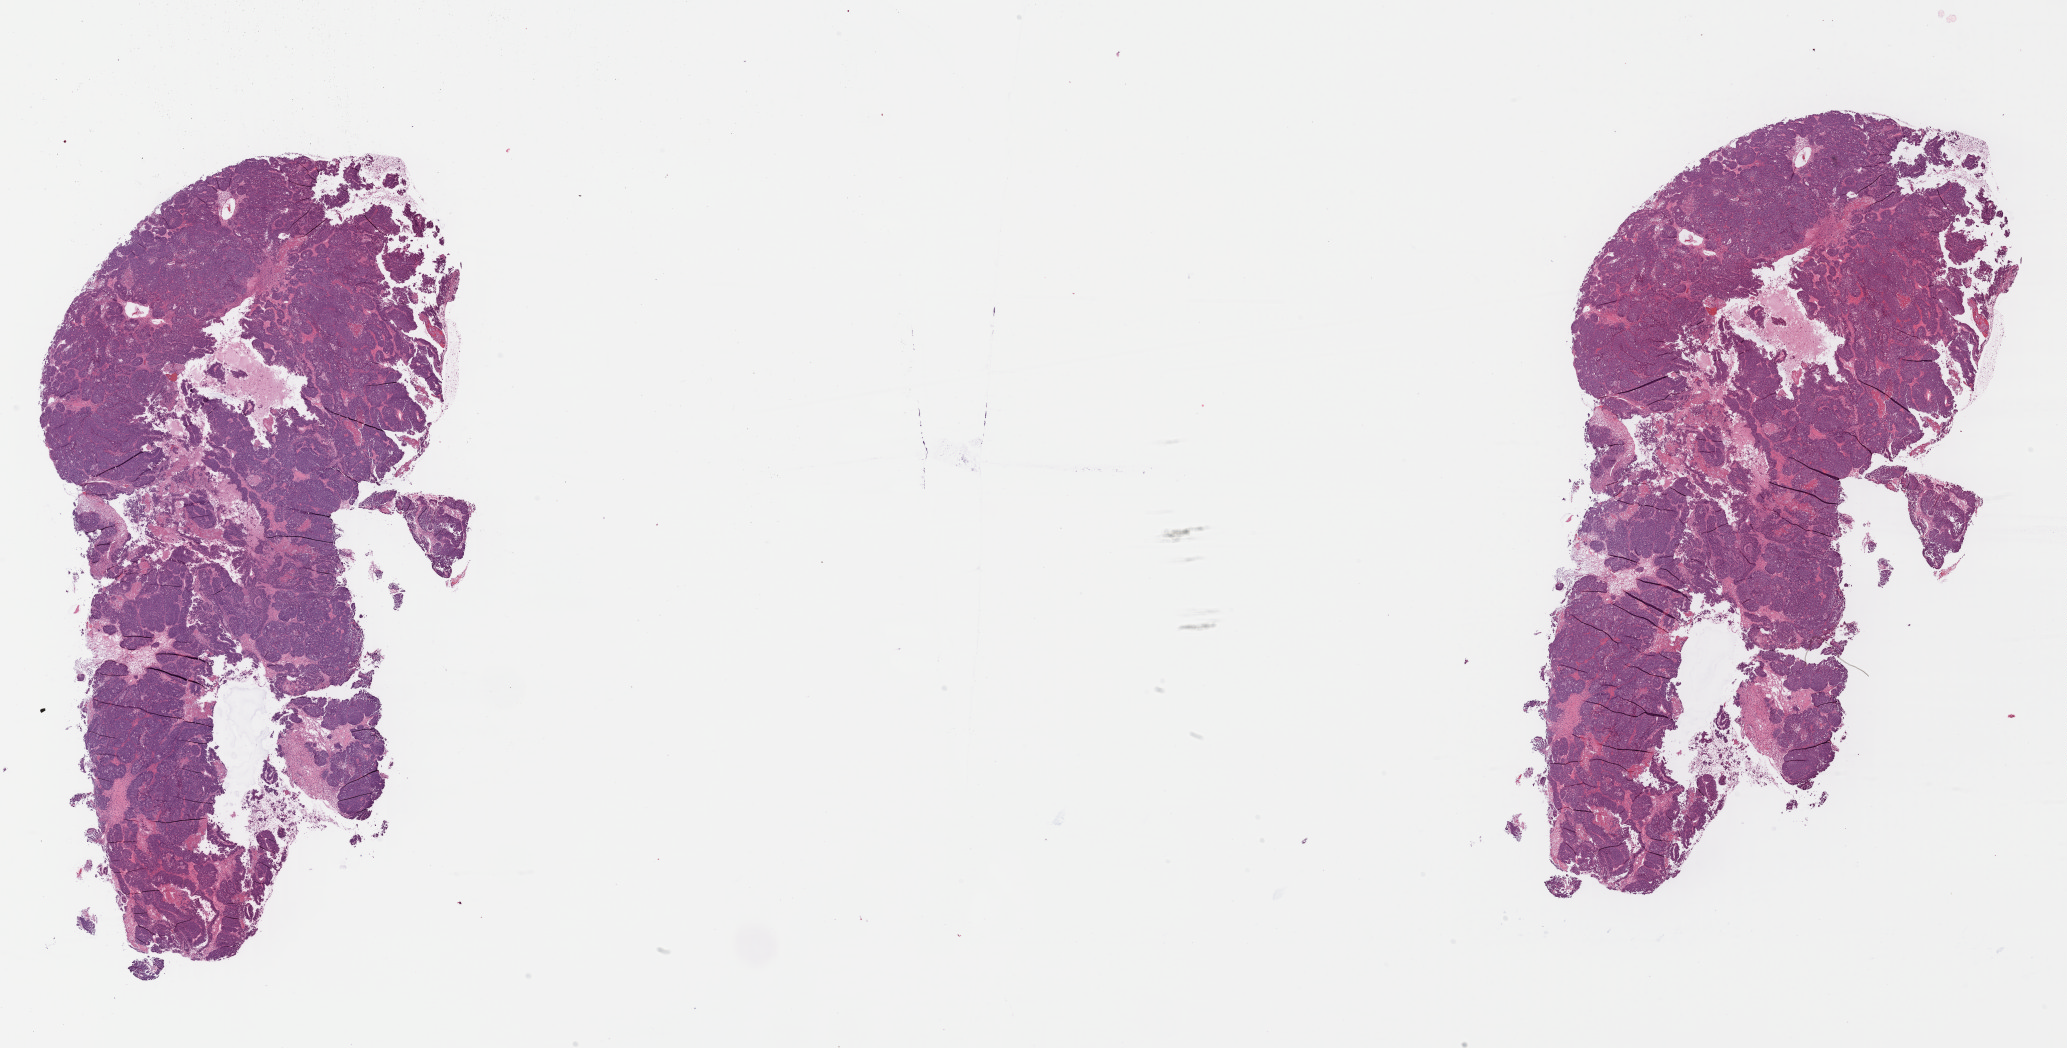
Digitized Hematoxylin and eosin (H&E) stained tissue section (whole slide), a low-resolution overview of the entire scanned area, about 32.5 x 16.5 mm (acquisition: 40x scan). Formalin-fixed paraffin-embedded (FFPE) diagnostic section. Primary tumour sample from the cervix. Patient: female, age at initial diagnosis 34 years. Histologic grade: G3 (poorly differentiated).
Diagnosis: Squamous cell carcinoma, NOS (ovary). FIGO stage: IVB.